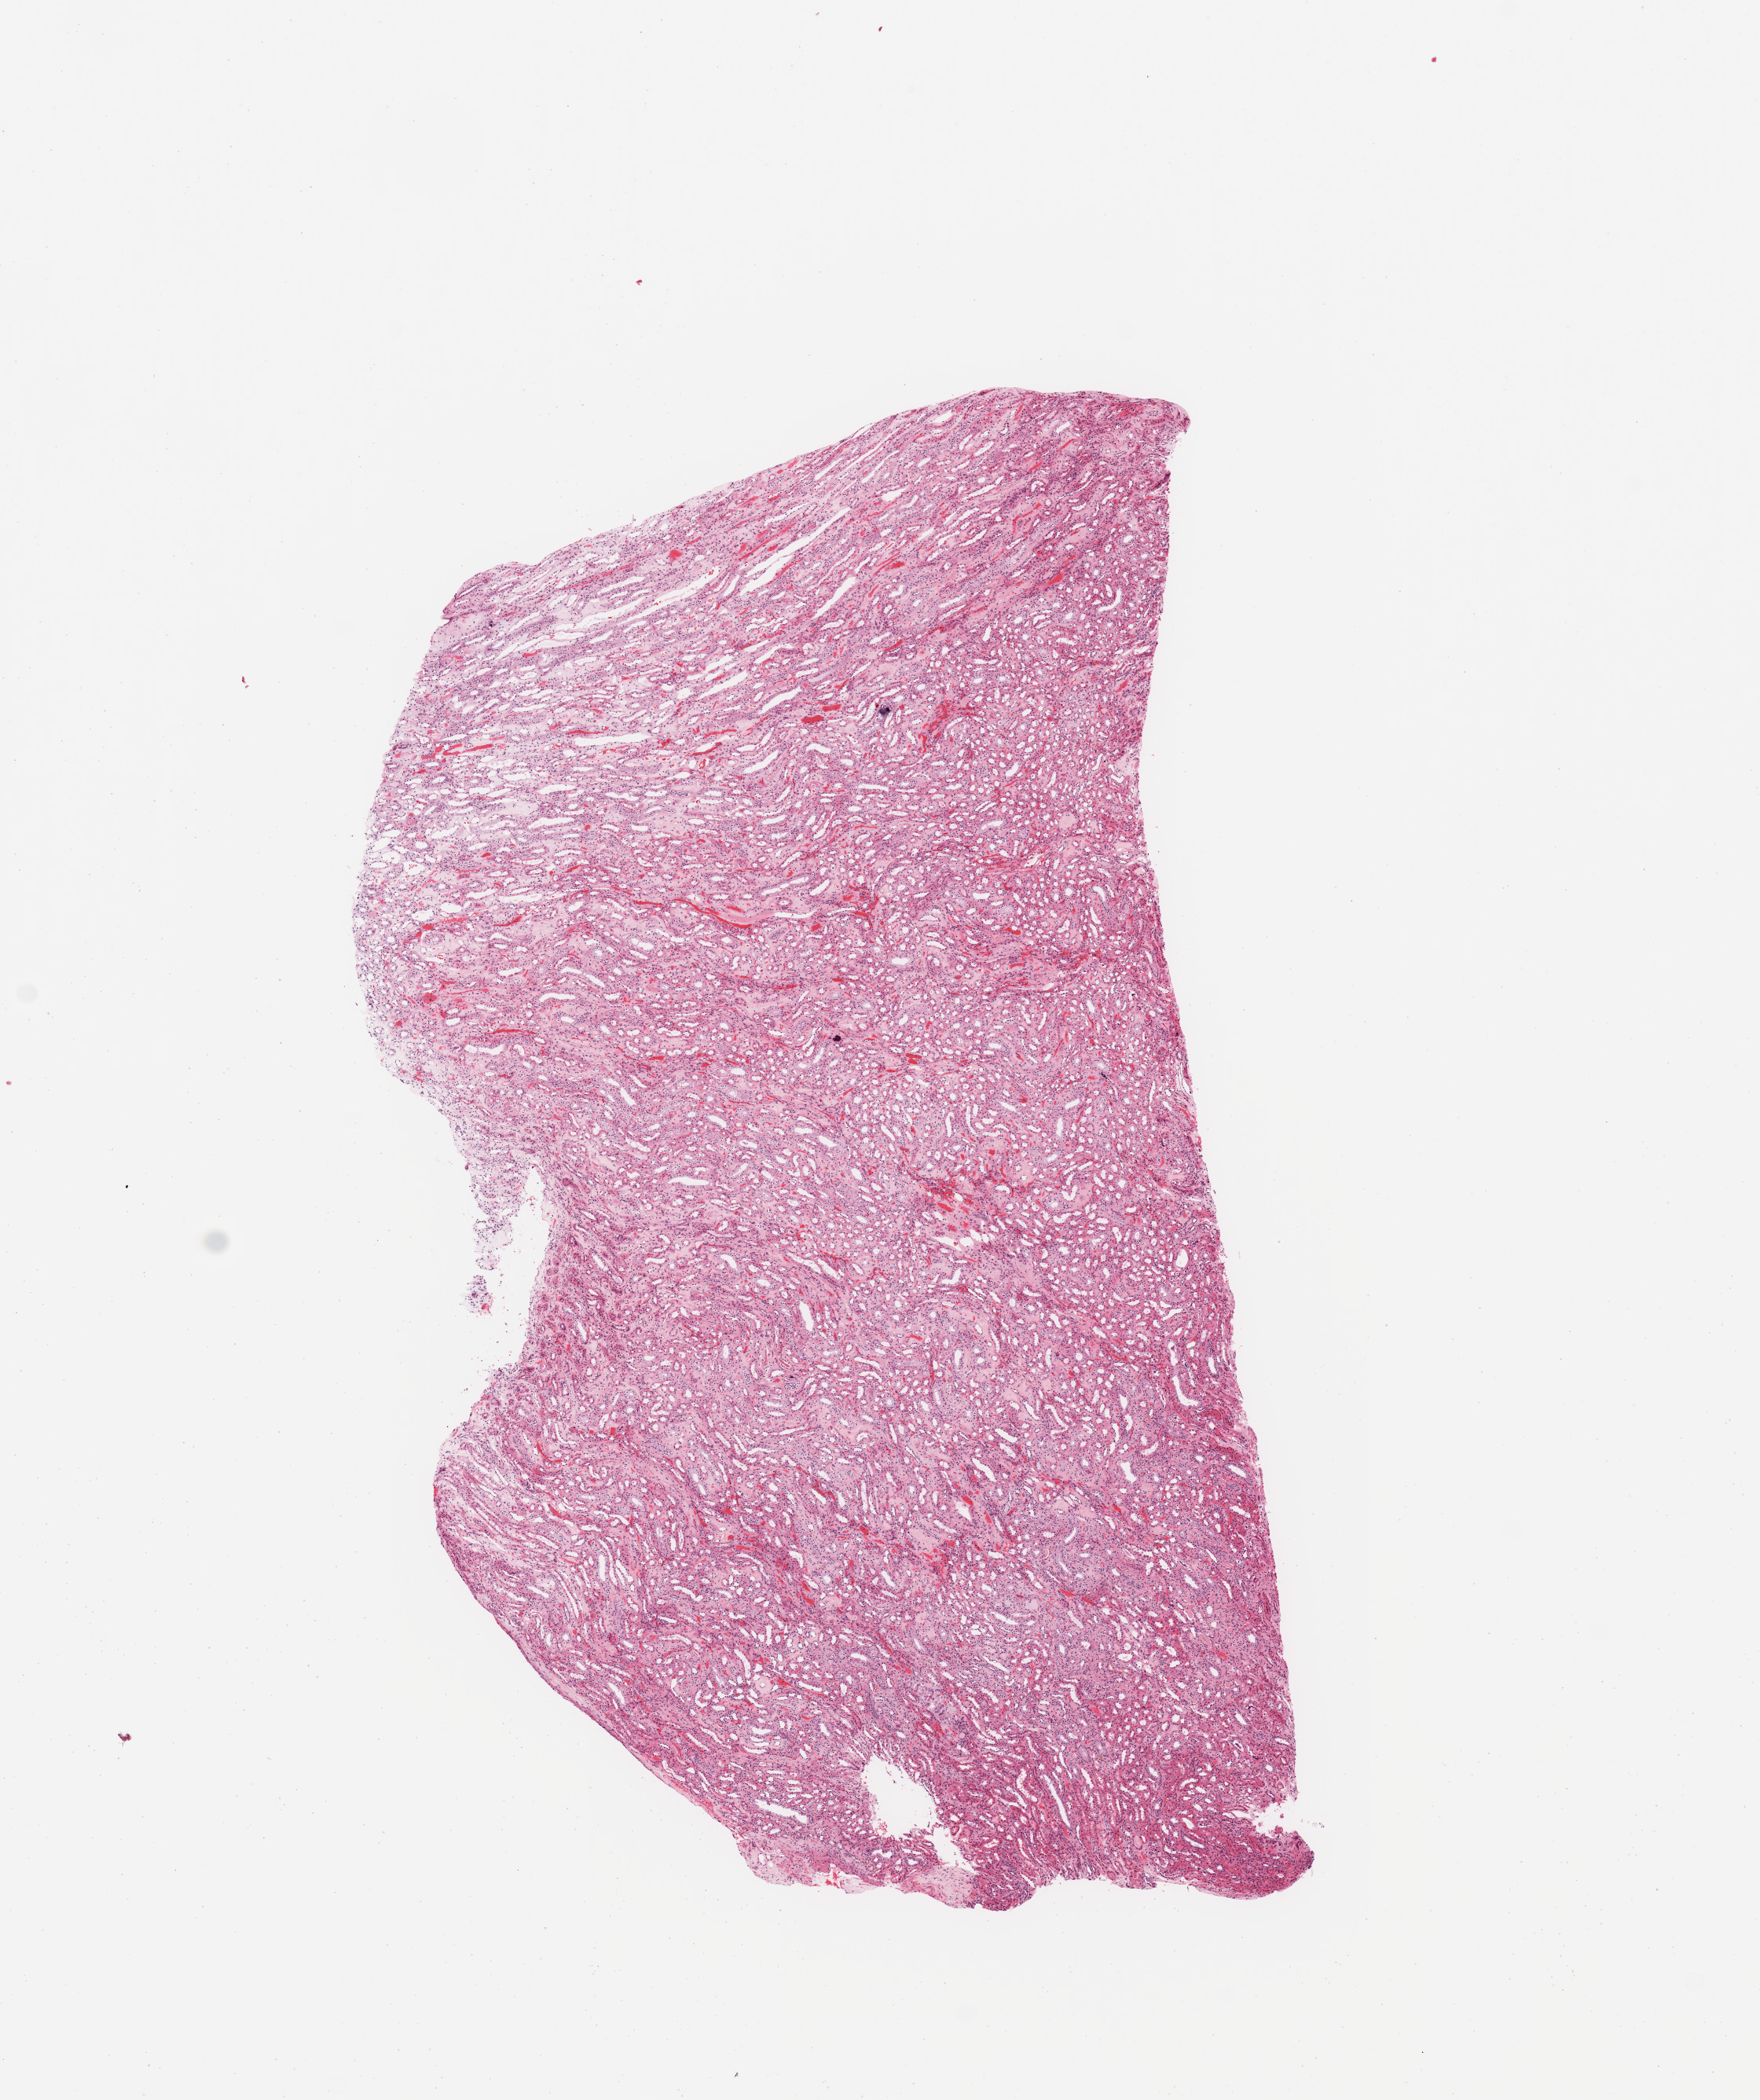
H&E whole-slide image — low-resolution overview of the scanned area, about 8.9 x 10.6 mm (slide scanned at 20x), normal (non-tumour) tissue sample, sampled site: kidney. 69-year-old female patient.
This section: normal (non-tumour) tissue from the same patient. Patient diagnosis: Renal cell carcinoma, NOS.